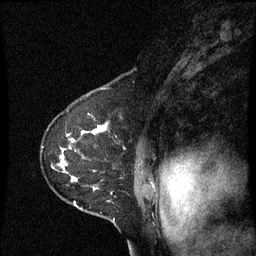
Breast MRI (dynamic contrast-enhanced), one sagittal slice; dynamic contrast-enhanced series, image 2 of 3 at this slice position (ordered by acquisition); 1.5 T; TE 4.2 ms, TR 8.9 ms; 256 × 256 image matrix, field of view 200 × 200 mm. Patient: female, 53 years. From the clinical record (not read from this slice): setting: breast cancer imaged before/during neoadjuvant chemotherapy; receptor status: HR-positive, HER2-negative.
Outlined on this slice (semi-automatically segmented with operator editing):
- analysis volume of interest (the breast-tissue region the enhancement analysis was run in; not a lesion): bounding box [x1, y1, x2, y2] px = [42, 100, 145, 221]
- tumour enhancement mask (voxels above the 70 % enhancement threshold inside the analysis volume of interest): [62, 126, 105, 181]